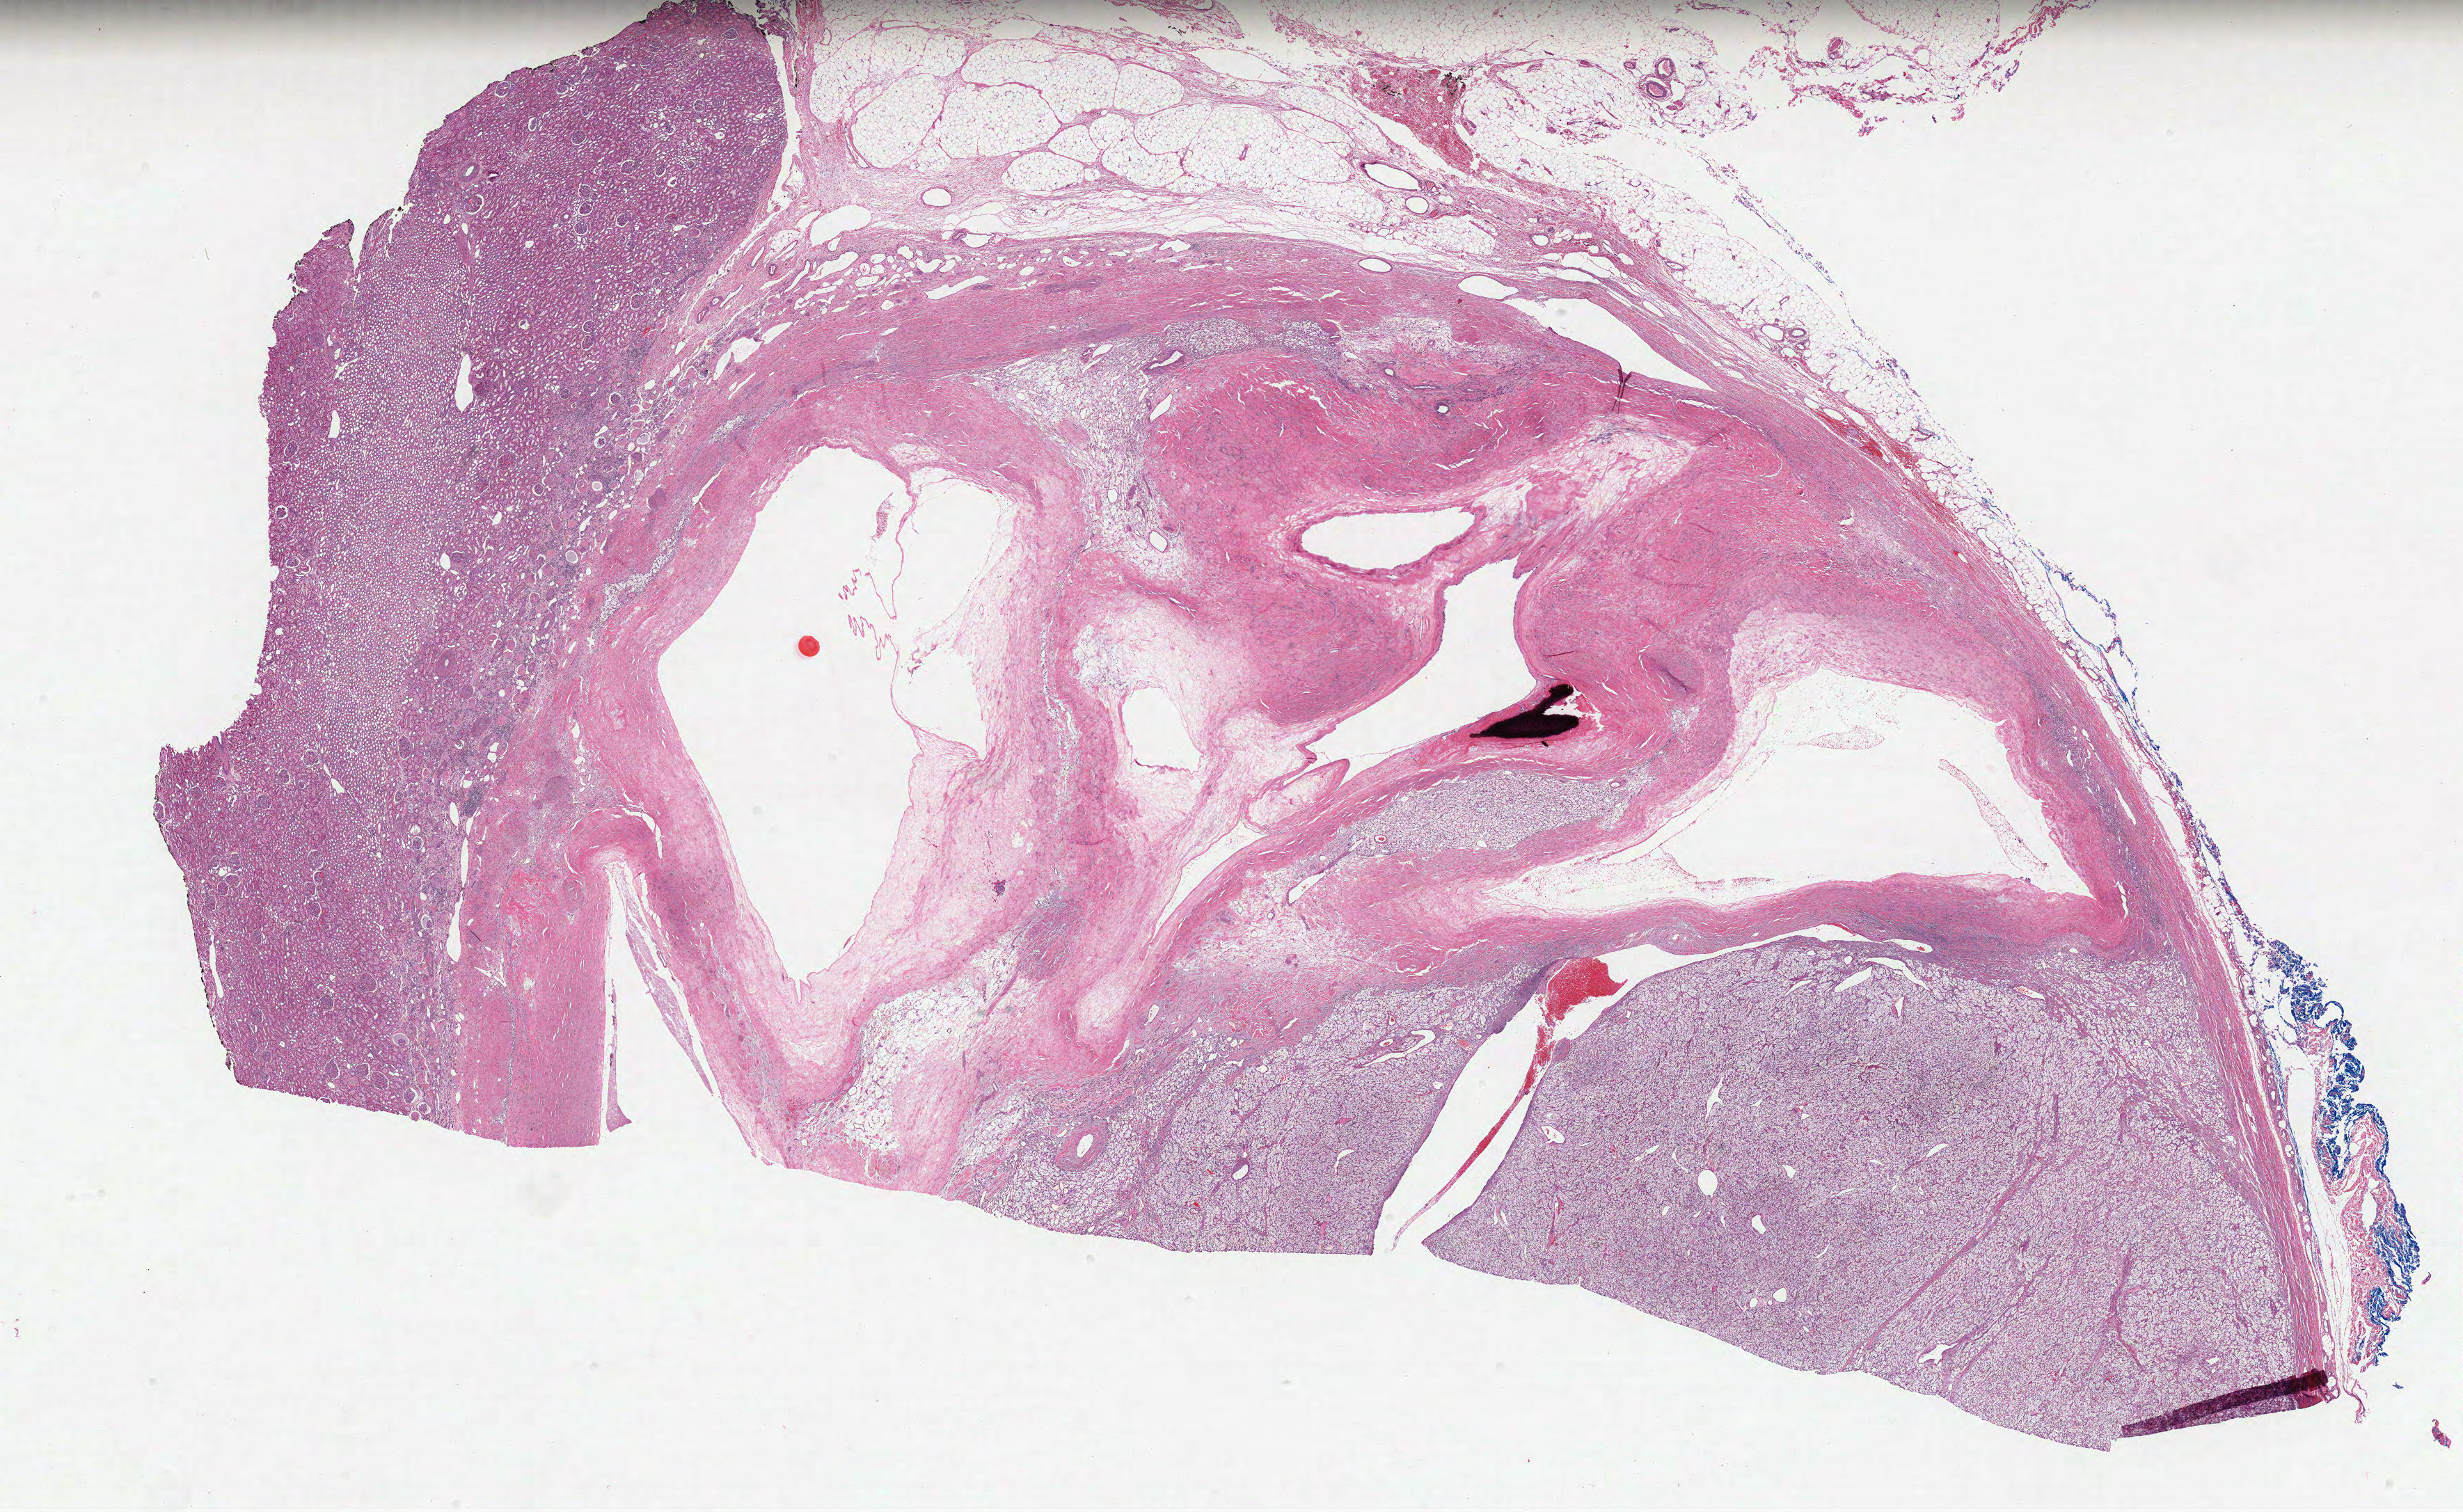
Whole-slide histology image, H&E, whole scanned area (about 28.3 x 17.4 mm, acquisition: 40x scan) shown as a low-resolution overview, formalin-fixed paraffin-embedded (FFPE) diagnostic section, kidney, primary tumour sample. Male, age 48 years at initial diagnosis.
Pathologic diagnosis: Clear cell adenocarcinoma, NOS.